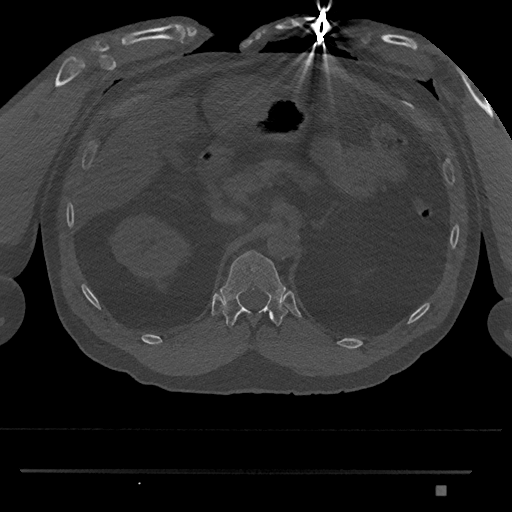
CT including the spine, one axial slice. Position 897 of 1134 along the scan axis. Reconstruction kernel Br40s/3. Bone window (W 1800 / L 400 HU). 0.5 mm slice thickness. 512 × 512 image matrix, field of view 429 × 429 mm. Male patient, age 65 years. From the clinical record (not read from this slice): primary cancer: prostate.
Structures marked on this image (semi-automatic segmentation, software-assisted and operator-edited):
- T12 vertebra: box from (x=220, y=250) to (x=288, y=328) px